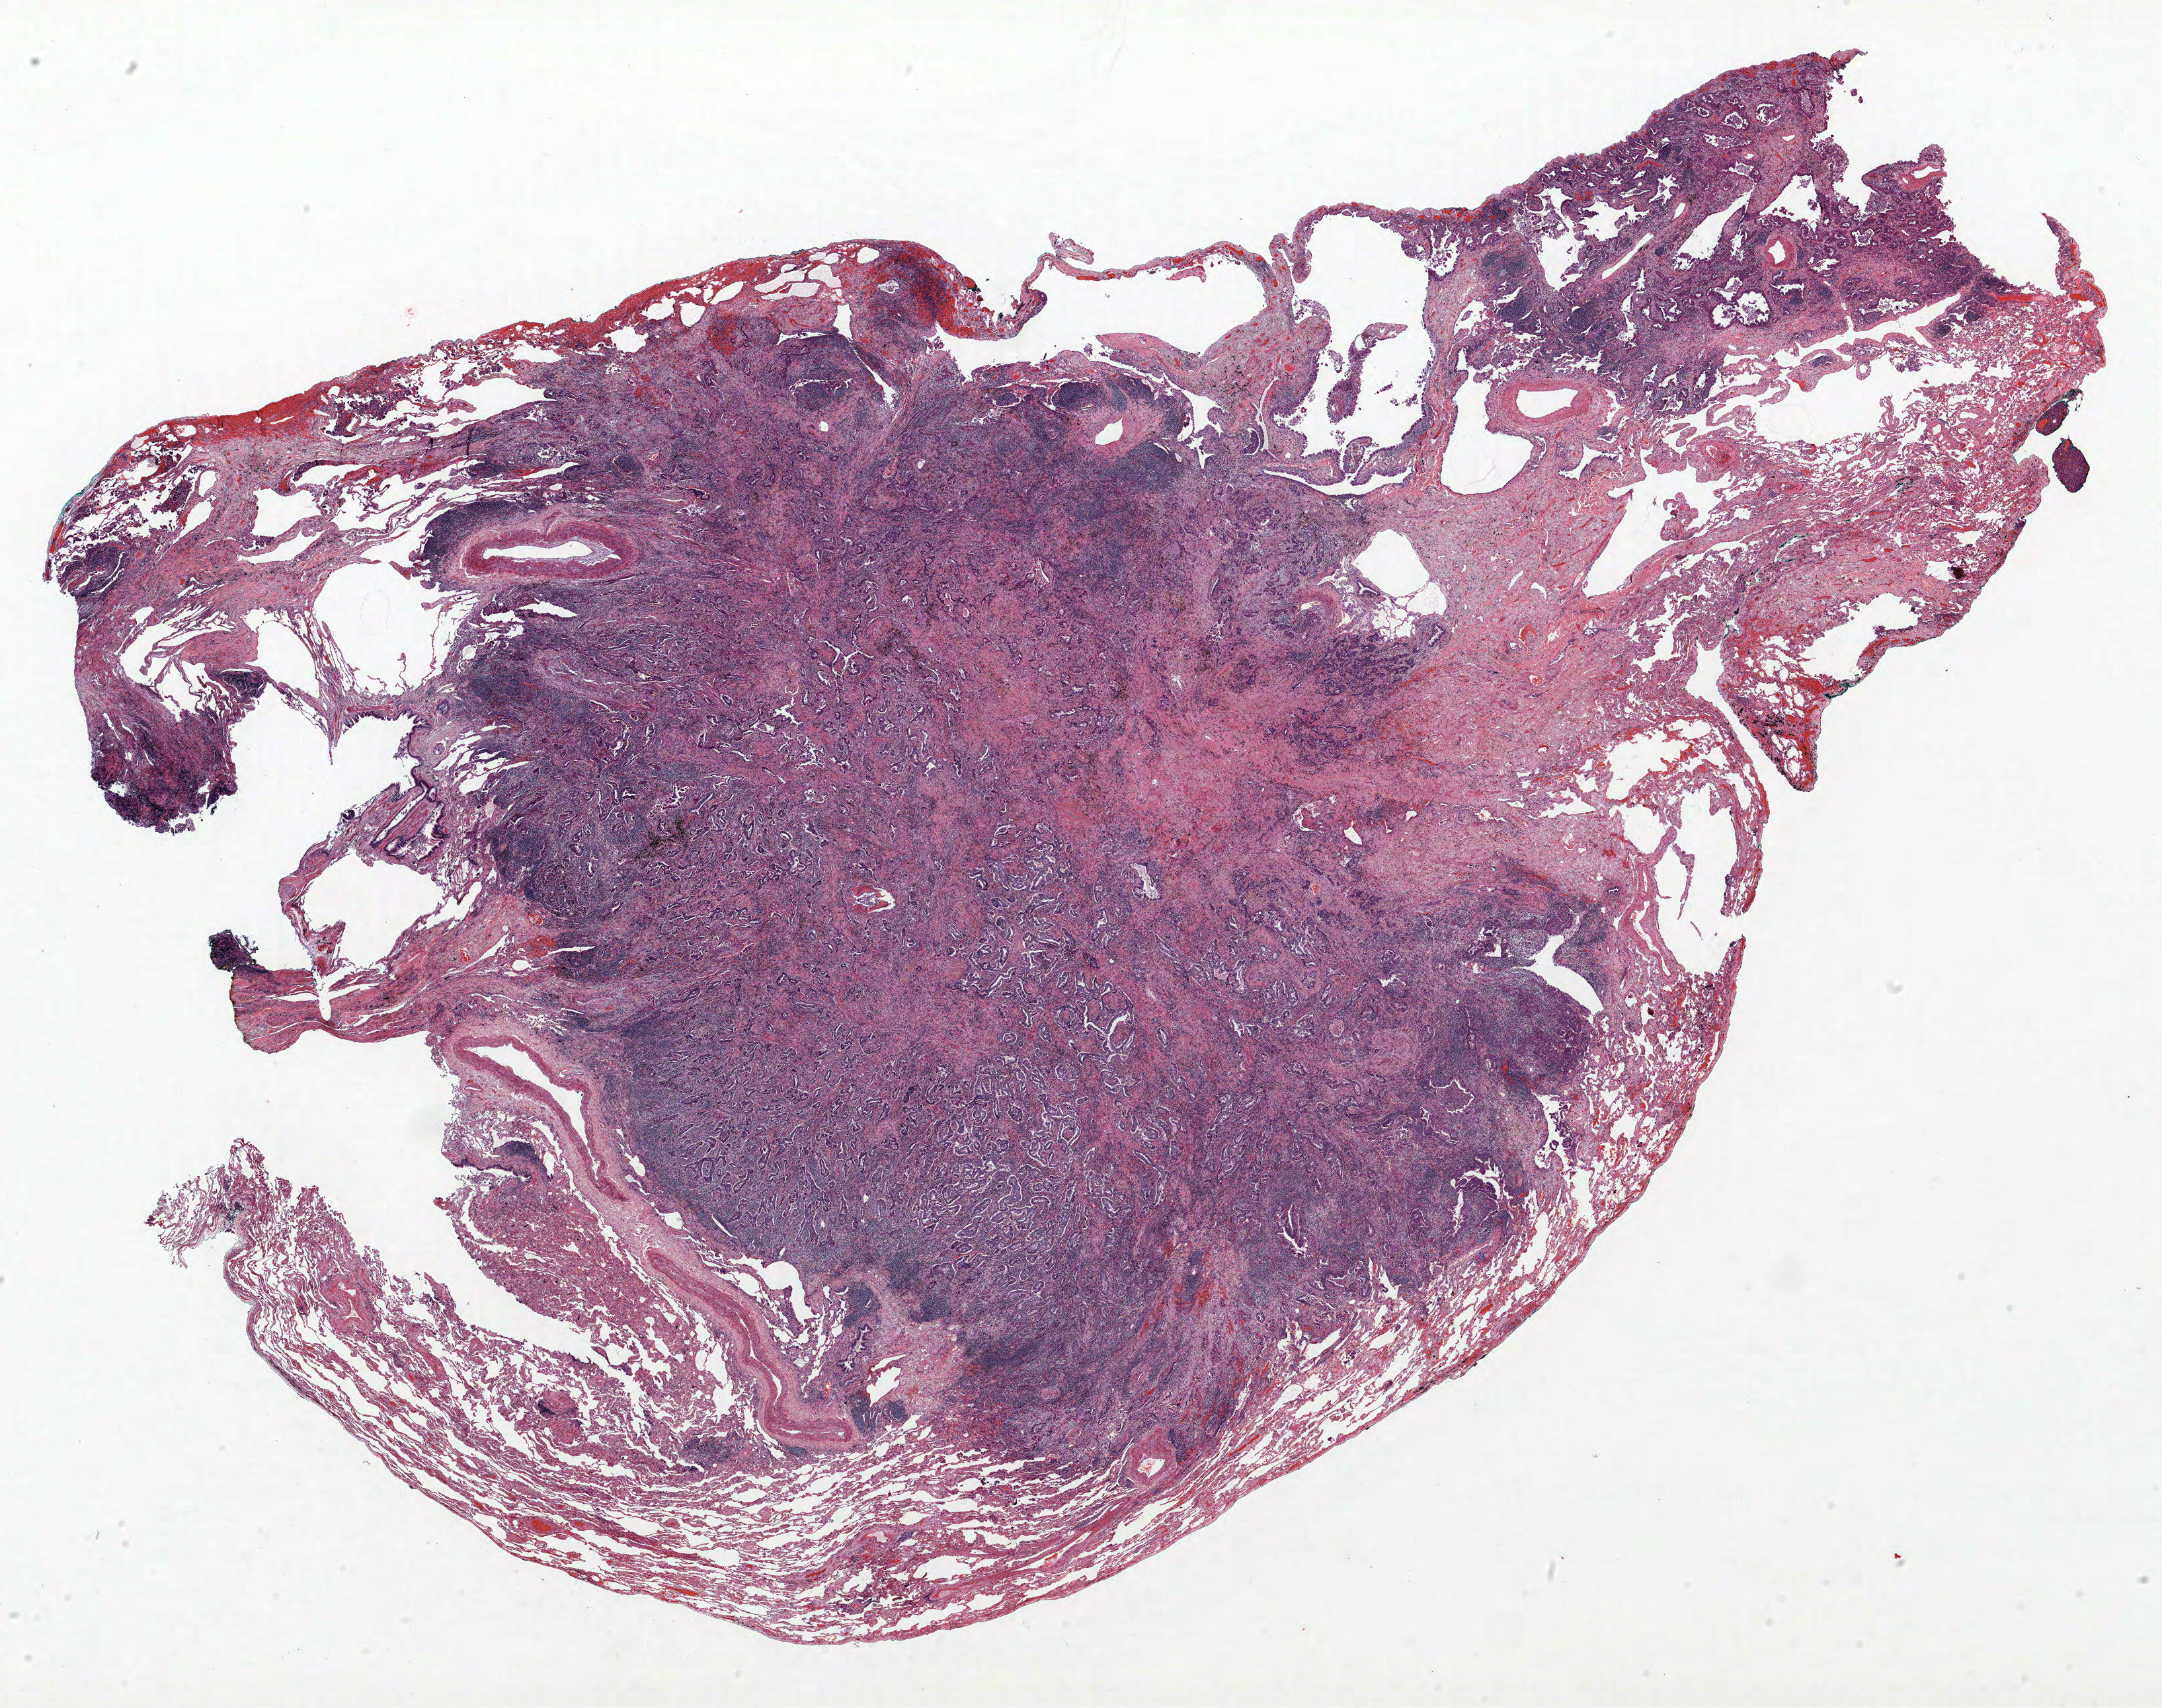
Whole-slide histology image, Hematoxylin and eosin (H&E) stained — whole scanned area (about 26.2 x 20.7 mm, from a 40x scan) shown as a low-resolution overview, formalin-fixed paraffin-embedded (FFPE) section, lung. Female patient, aged 64 at enrolment. Former smoker at enrolment. Grade: moderately differentiated (G2).
Participant's lung-cancer diagnosis: Adenocarcinoma, NOS. Tumour size (pathology): 17 mm. Primary tumour location (clinical record): left lower lobe. Stage (AJCC 6th edition): IA.